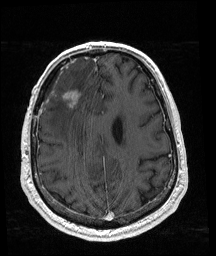
Brain MRI from a brain-tumour surgery series, one axial slice. Position 65 of 192 along the scan axis. T1-weighted post-contrast. 216 × 256 image matrix, field of view 211 × 250 mm. Case-level facts recorded for this patient, not image findings: histopathology: Glioblastoma; WHO grade: 4.
Annotated regions visible in this slice (expert manual segmentation):
- tumour: bounding box [x1, y1, x2, y2] px = [62, 91, 80, 106]